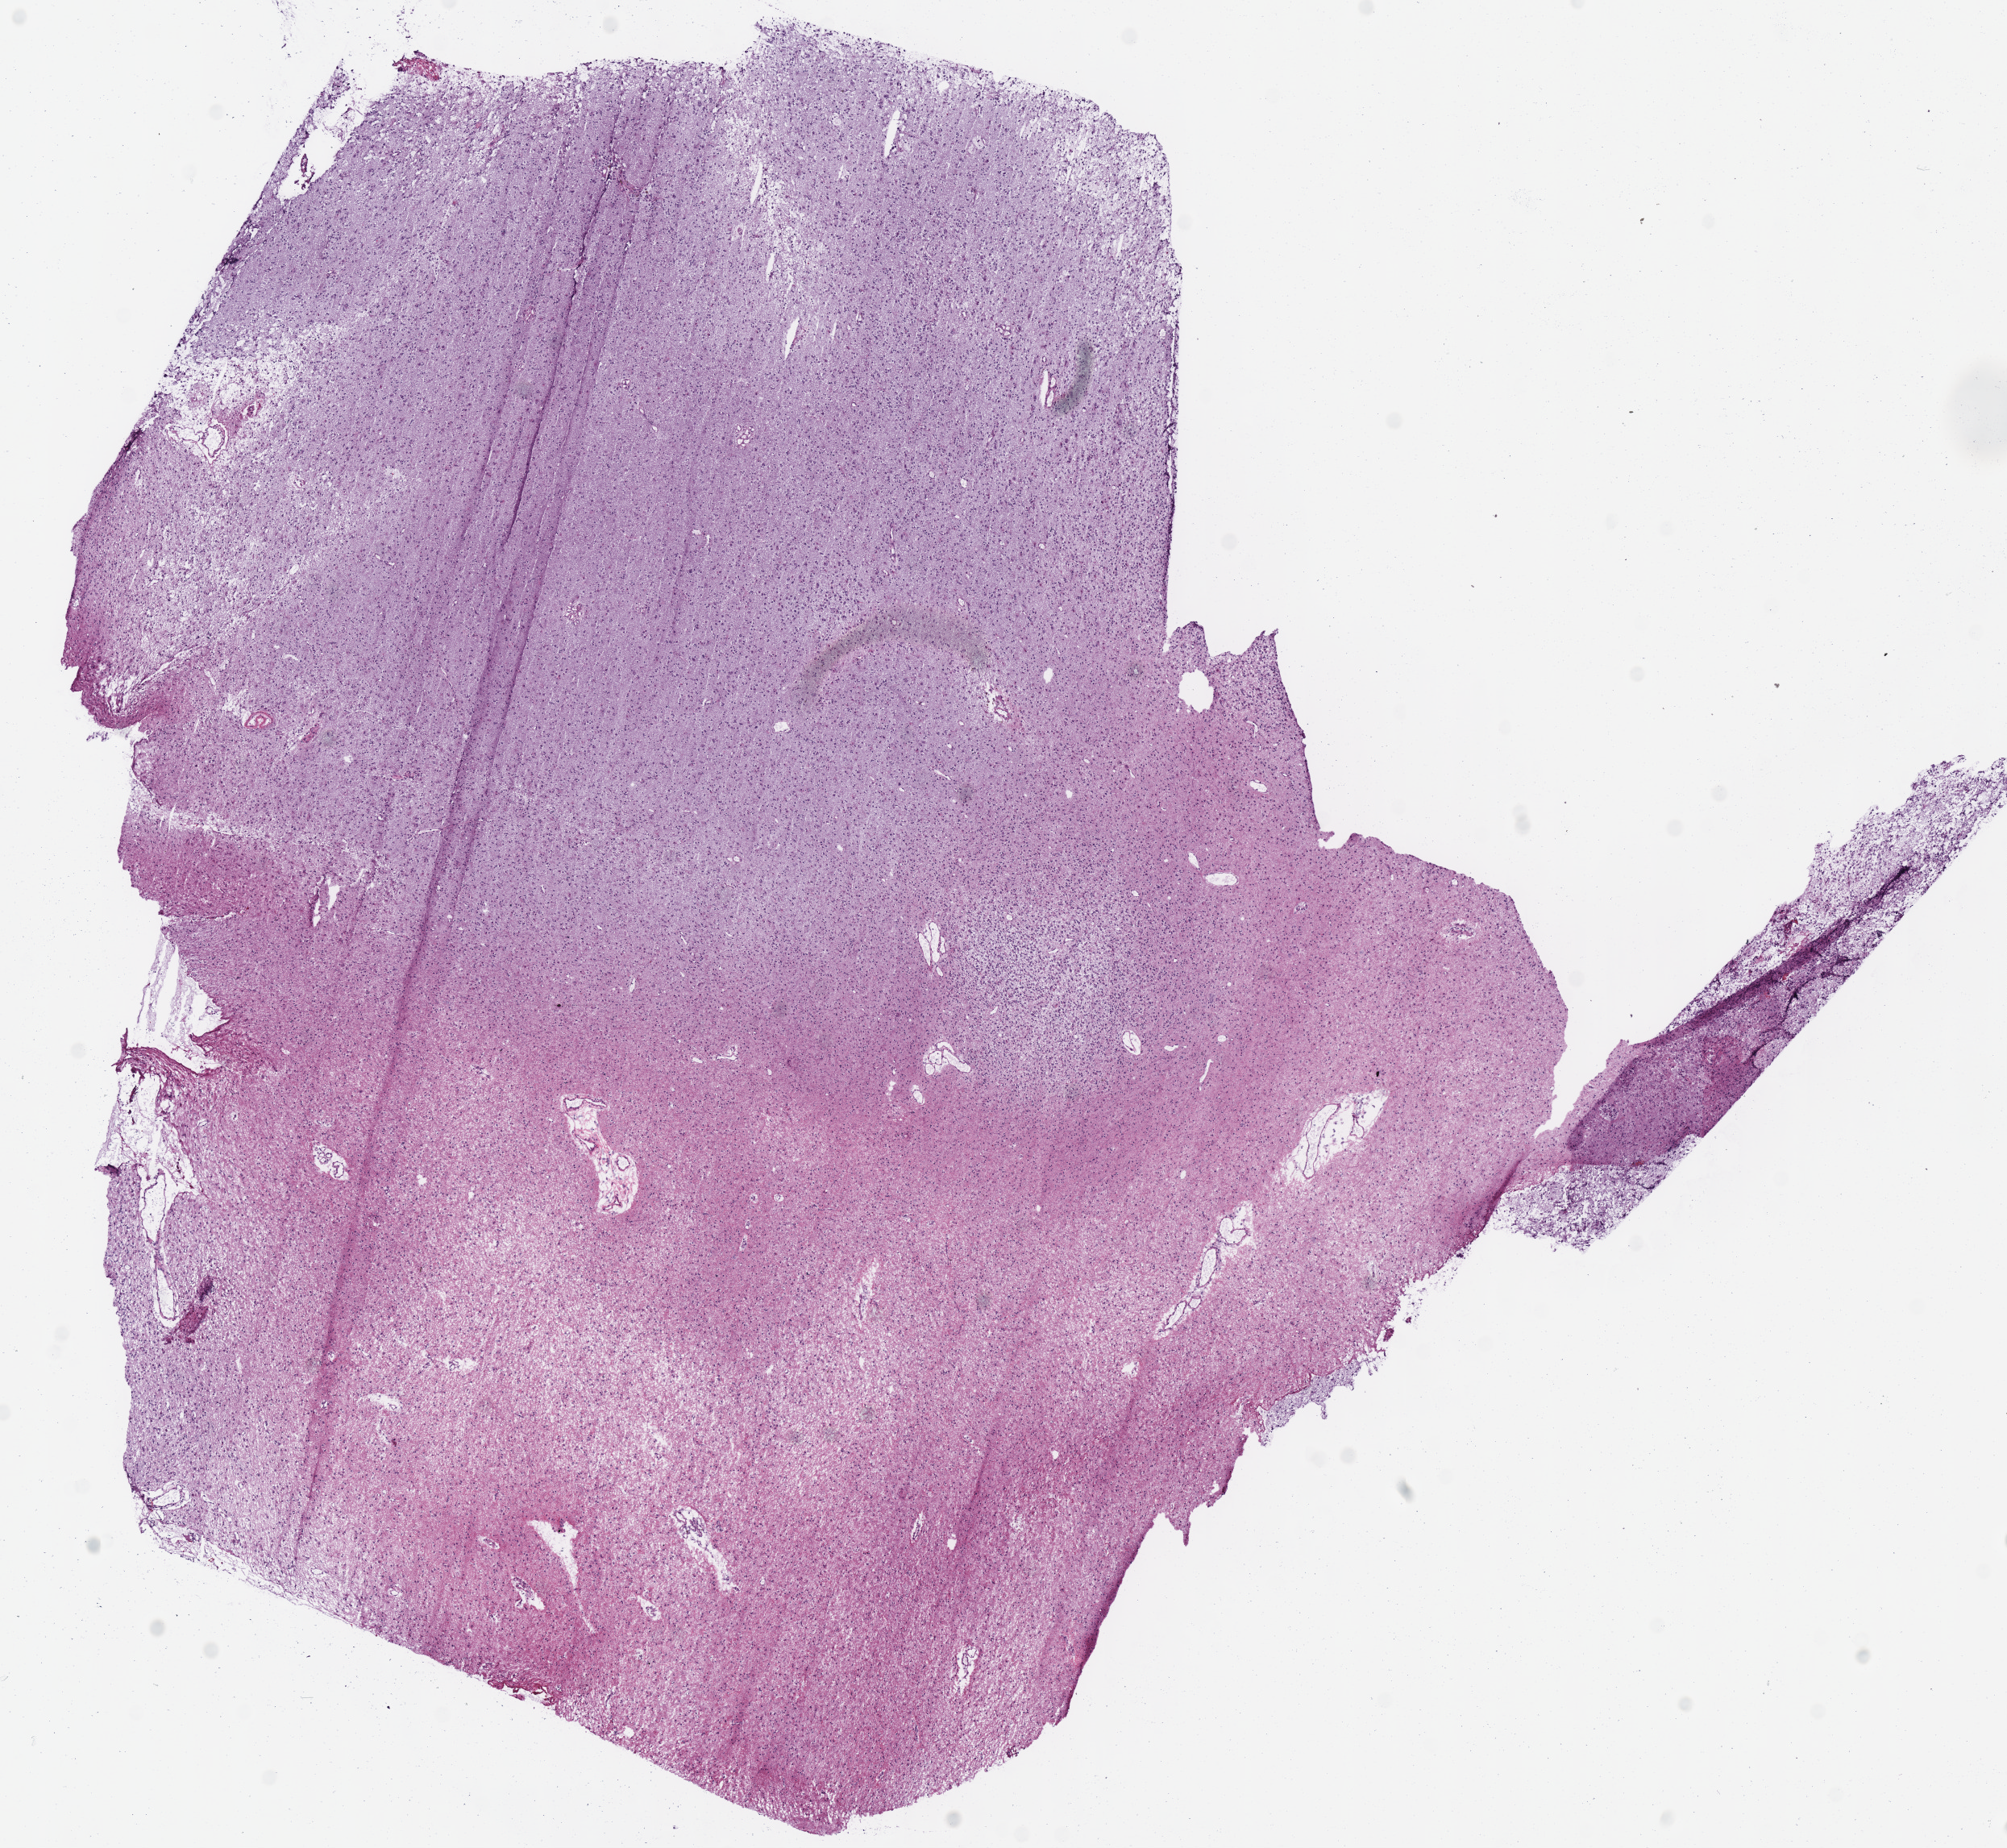
Digitized Hematoxylin and eosin (H&E) stained tissue section (whole slide), shown as a low-resolution overview of the whole scanned area (about 9.8 x 9.0 mm, slide scanned at 40x); frozen section from the bottom of the tissue portion; primary tumour sample from the brain. Male patient; age at initial diagnosis 62 years. Histologic grade: G3 (poorly differentiated). Slide review estimates, as recorded: tumour cells 100%, tumour nuclei 75%, normal cells 0%, stromal cells 0%, necrosis 0%.
Diagnosis: Mixed glioma.